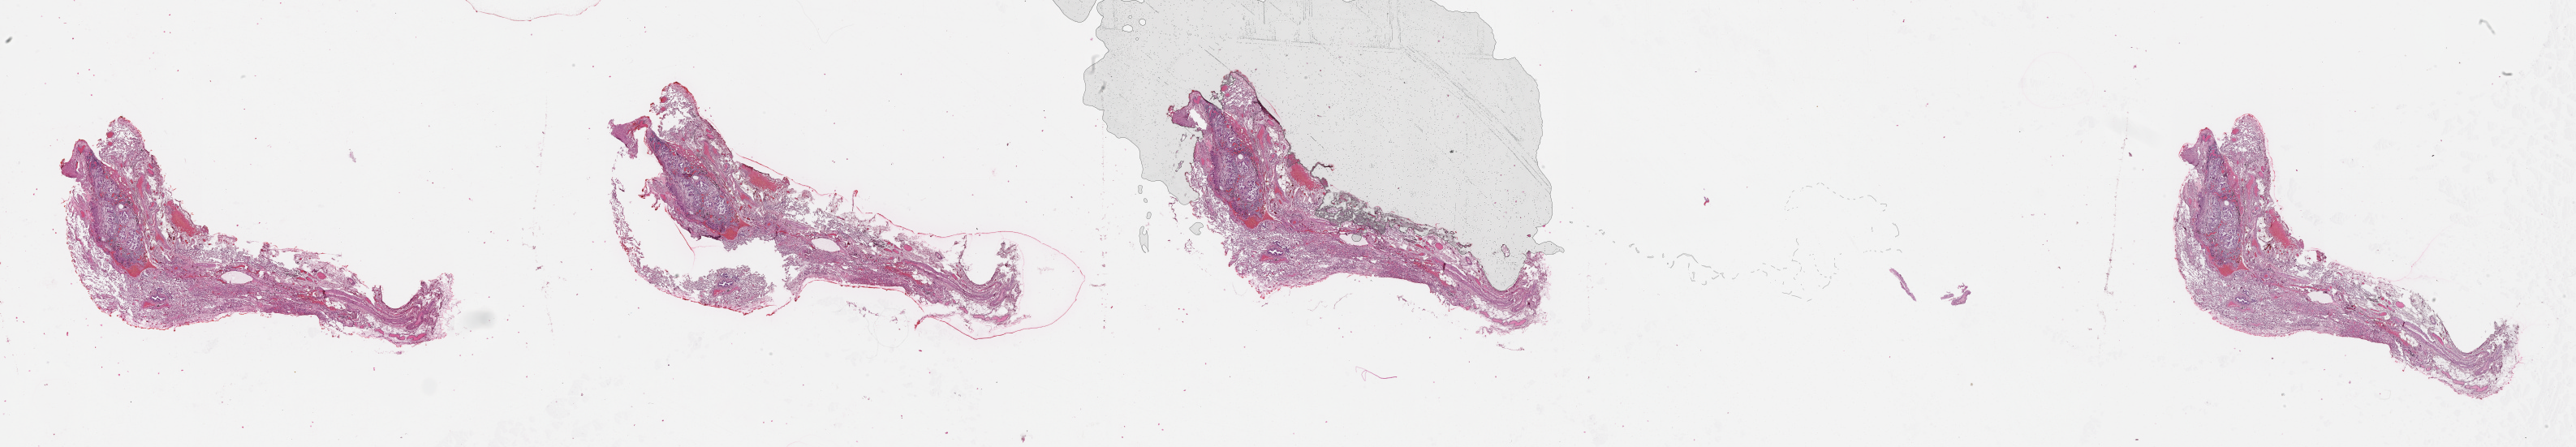
Hematoxylin and eosin (H&E) stained whole-slide image — low-resolution overview of the scanned area, about 51.1 x 8.9 mm; lung, tissue type not recorded.
Patient diagnosis (cohort enrolment): lung adenocarcinoma (lung).